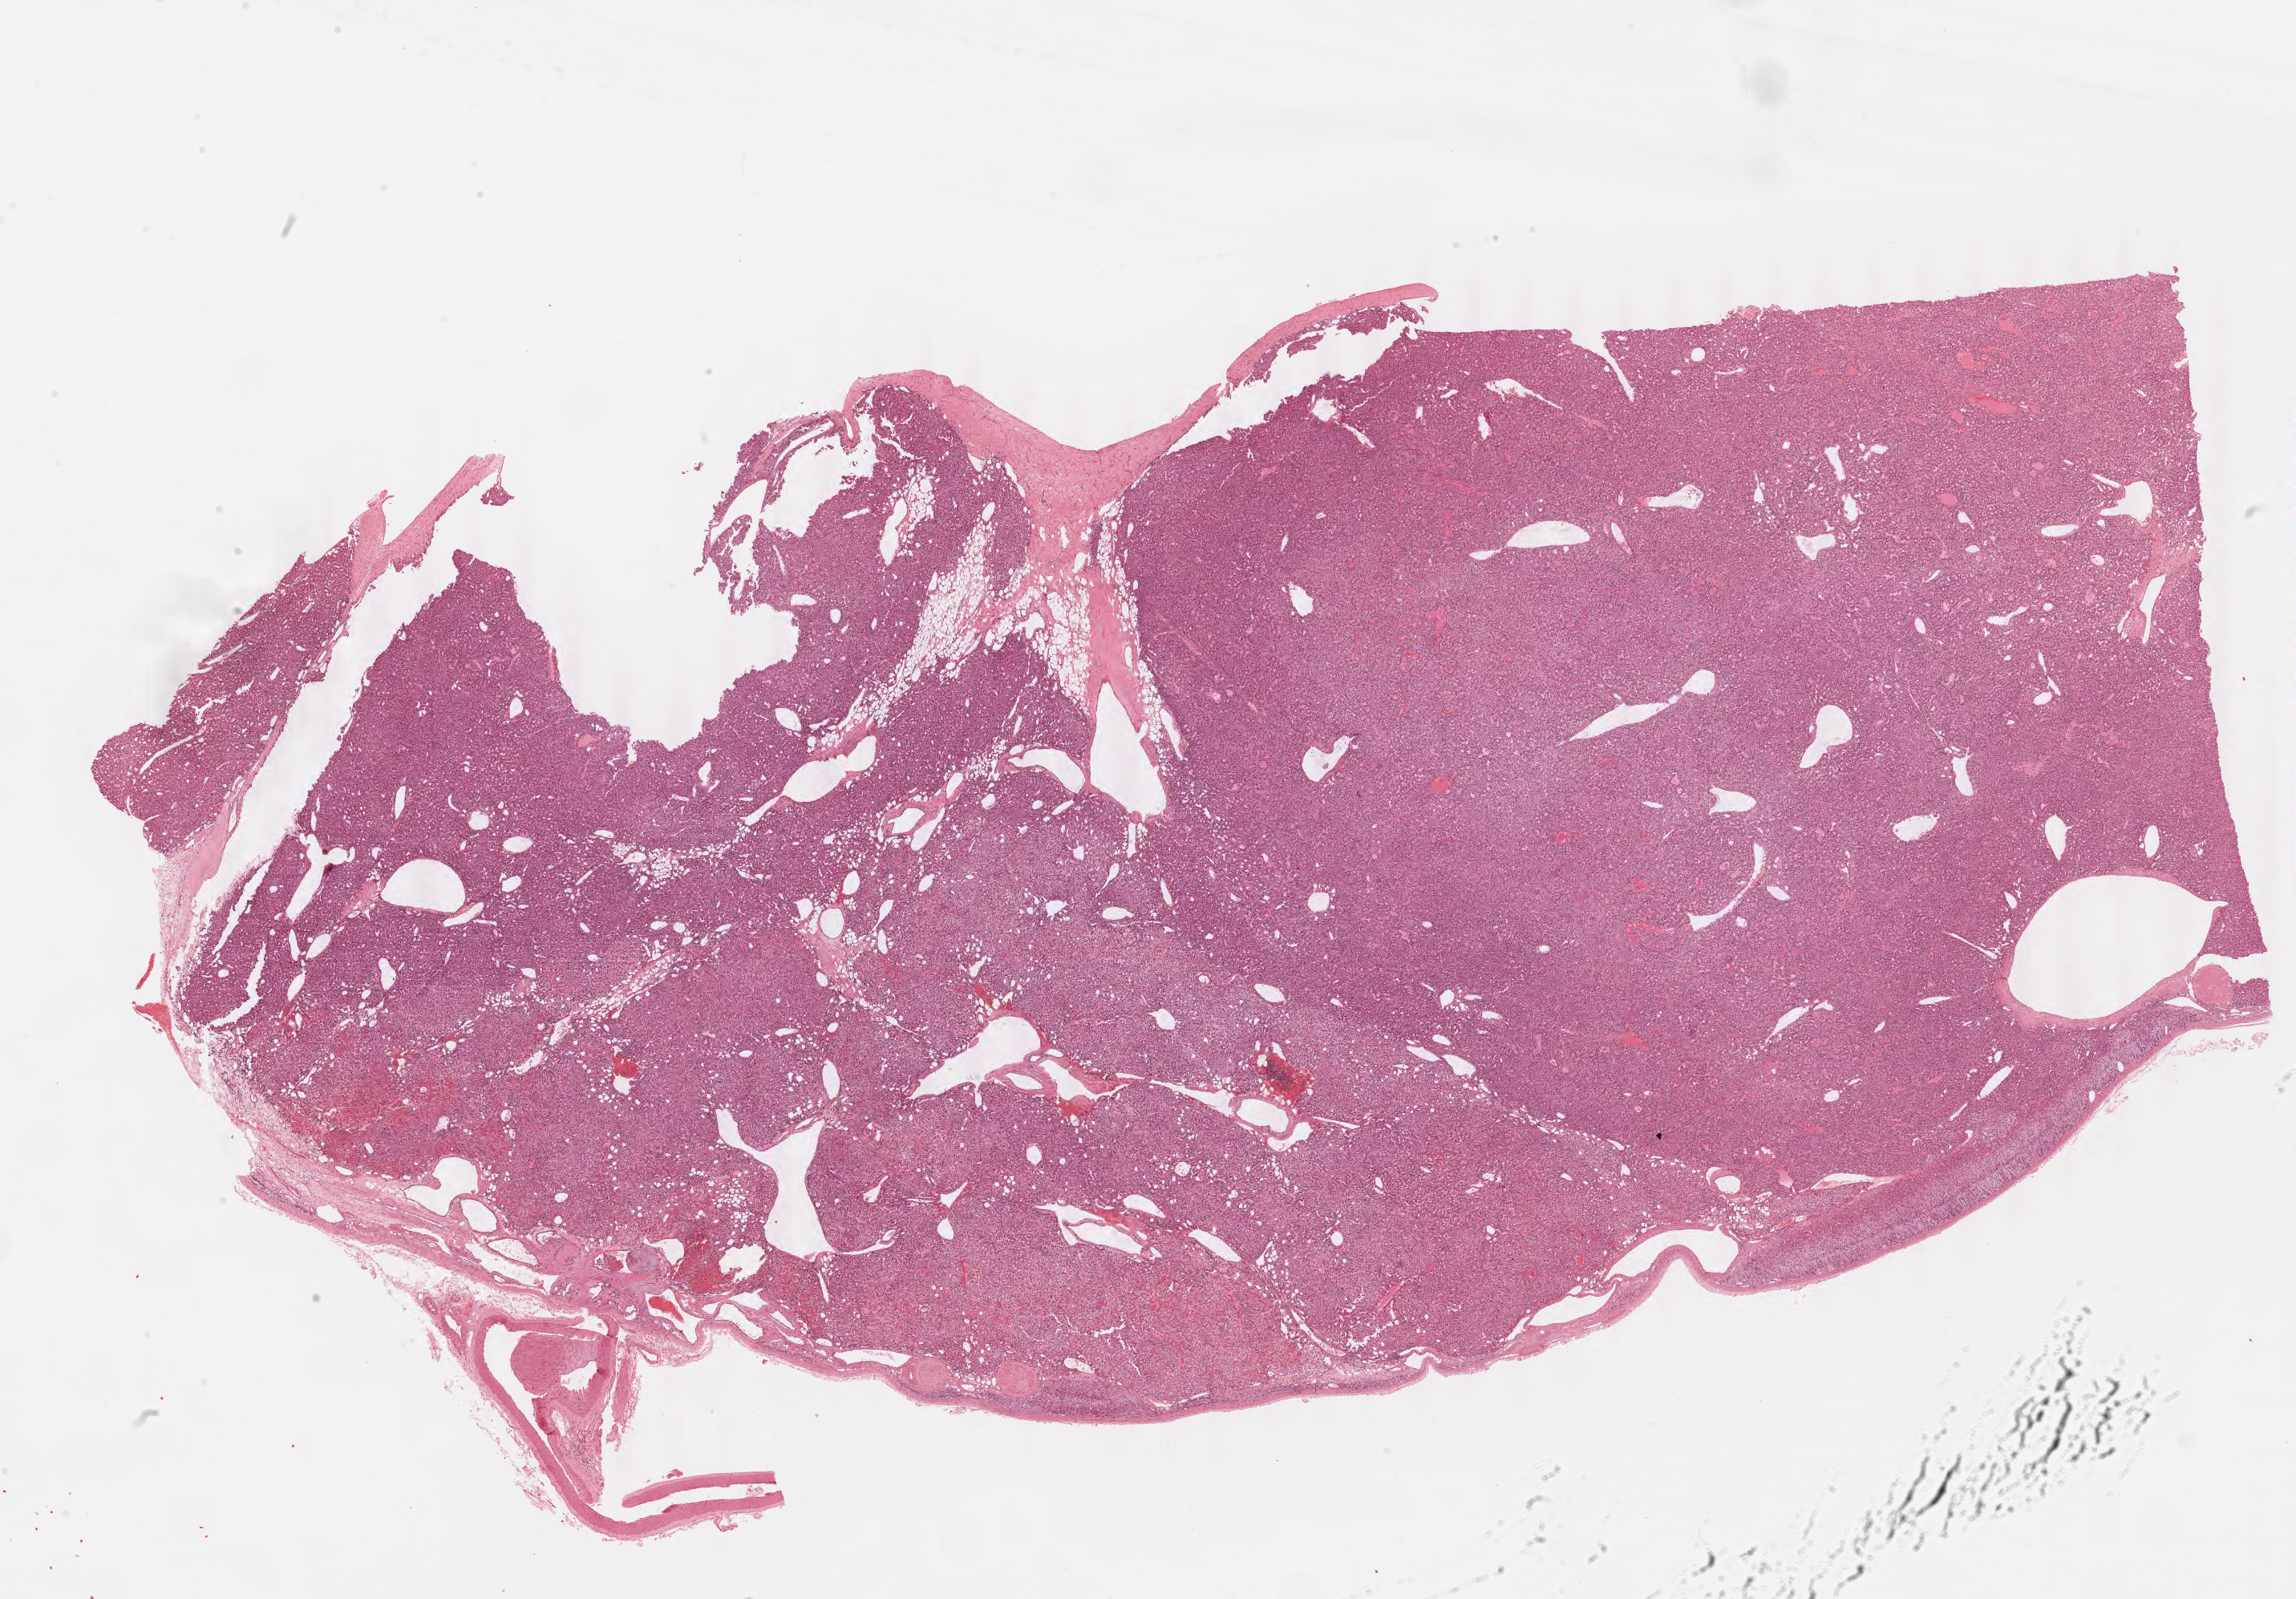
Digitized H&E tissue section (whole slide), shown as a low-resolution overview of the whole scanned area (about 22.6 x 15.8 mm, slide scanned at 40x); FFPE section; adrenal cortex, primary tumour sample. Female, age 27 years at initial diagnosis.
Pathologic diagnosis: Adrenal cortical carcinoma (cortex of adrenal gland).